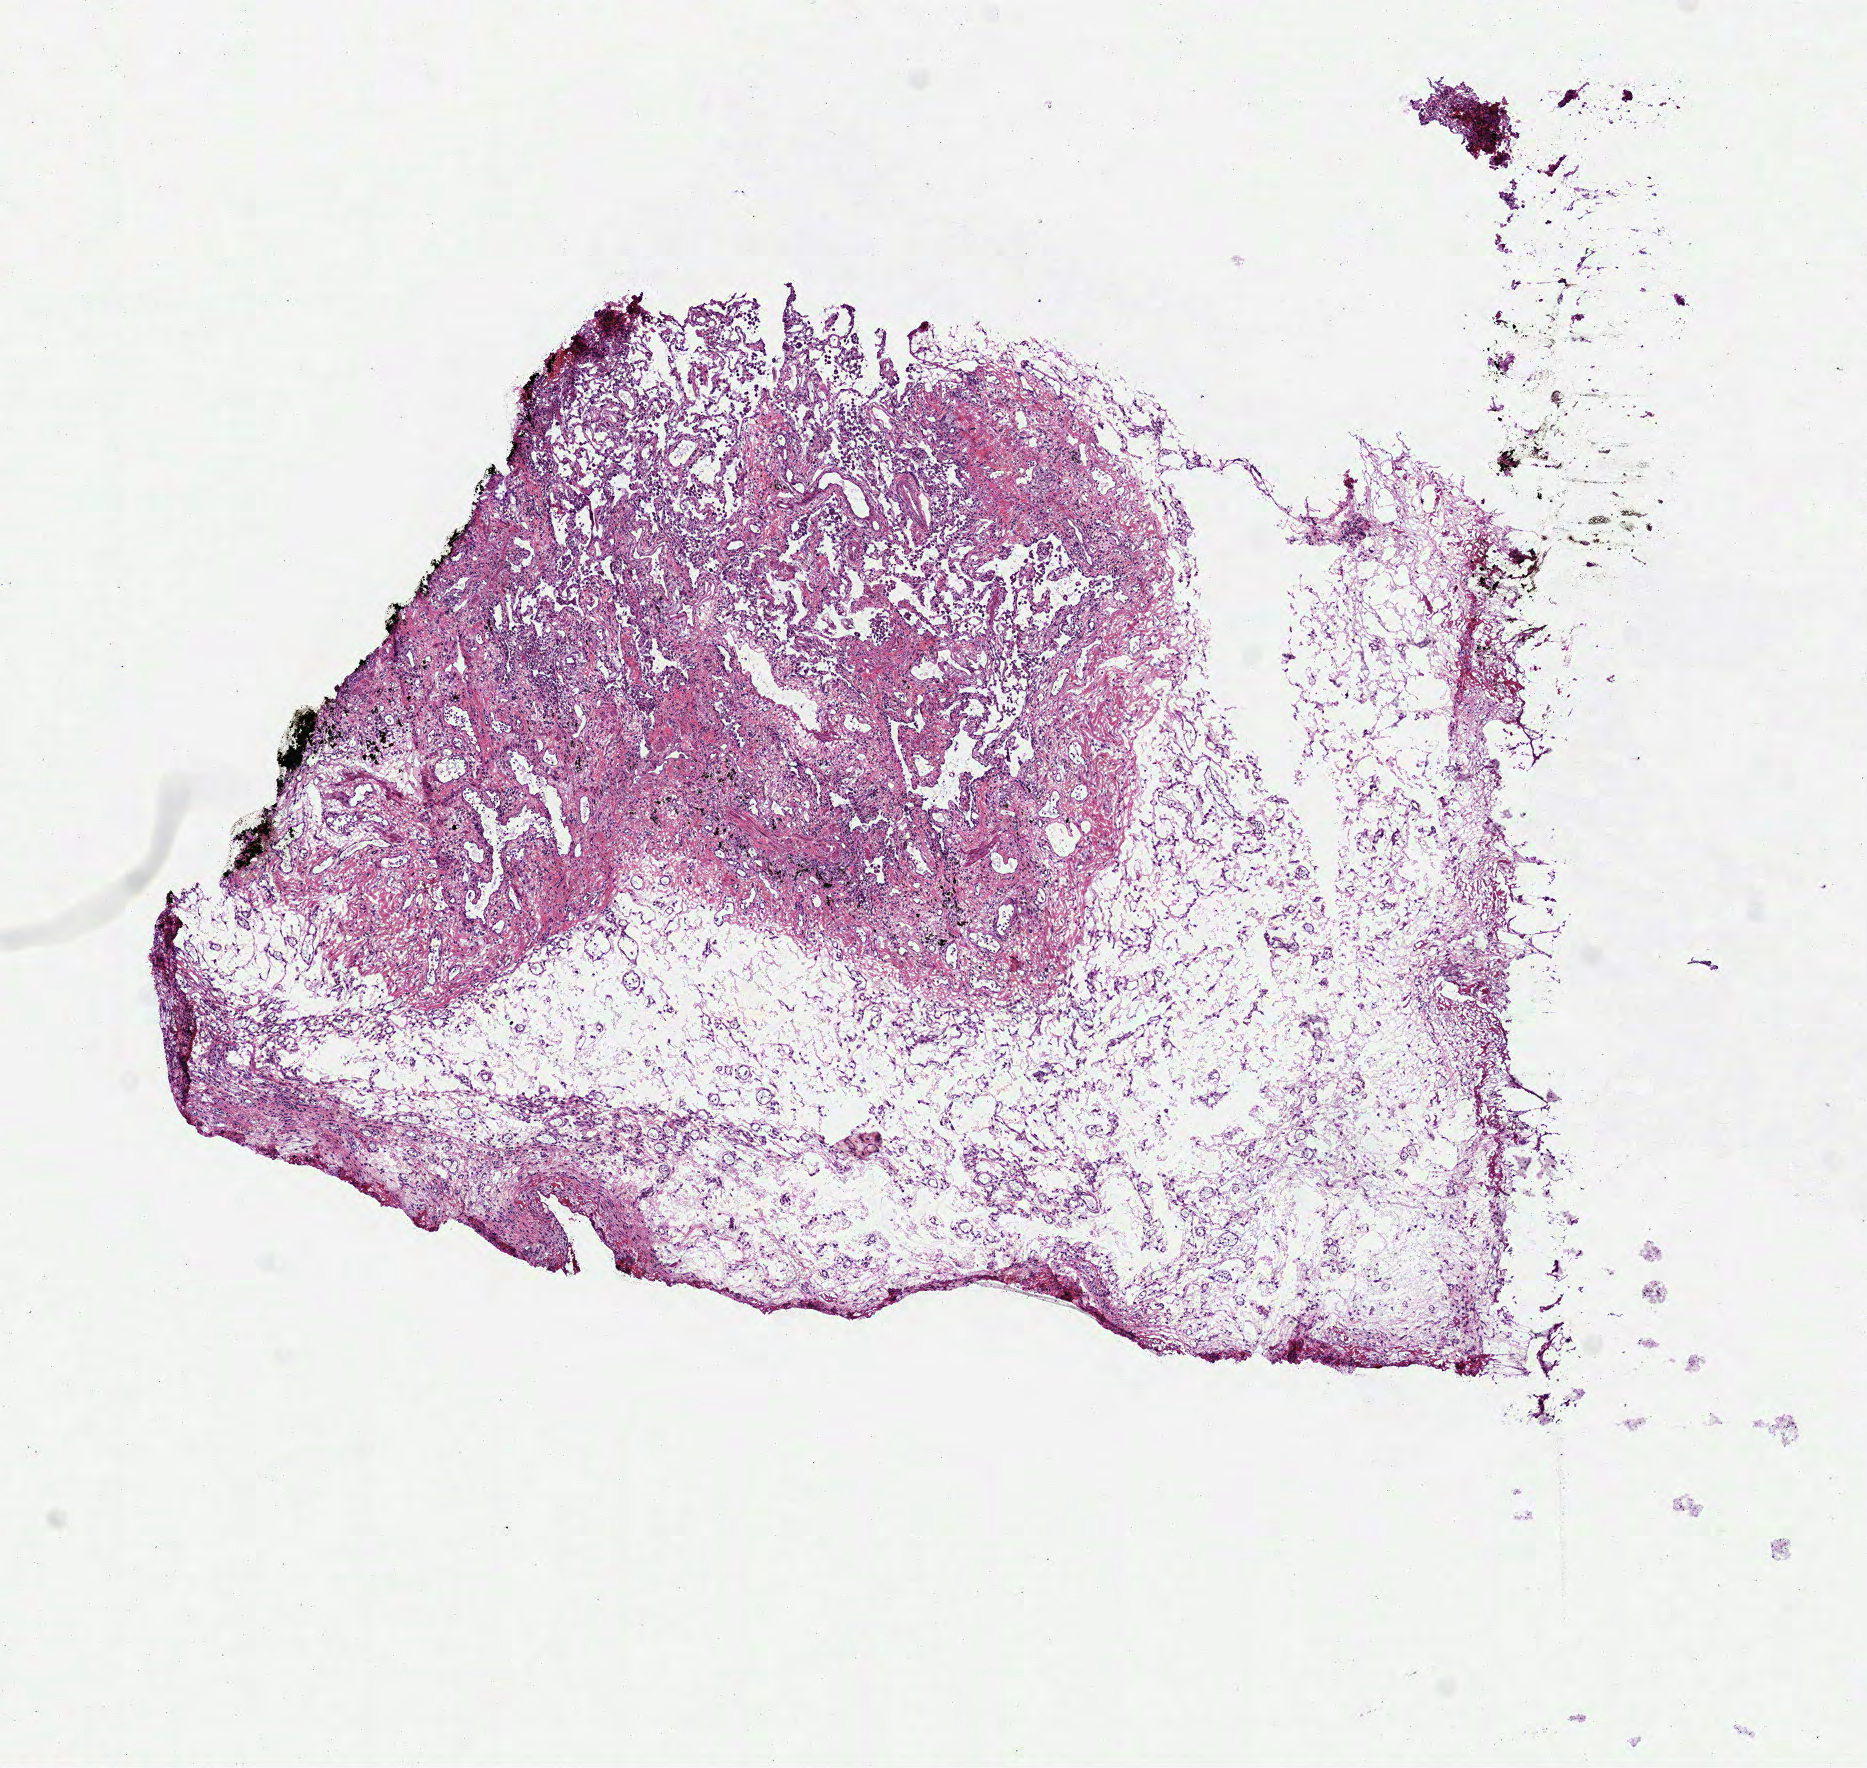
Digitized H&E tissue section (whole slide), whole scanned area (about 7.5 x 7.1 mm) shown as a low-resolution overview, frozen section, sample: solid tissue normal (non-tumour tissue), lung. Male patient; age at initial diagnosis 68 years.
This section: solid tissue normal (non-tumour) sample from the same patient. Patient diagnosis: Squamous cell carcinoma, keratinizing, NOS (lower lobe, lung).